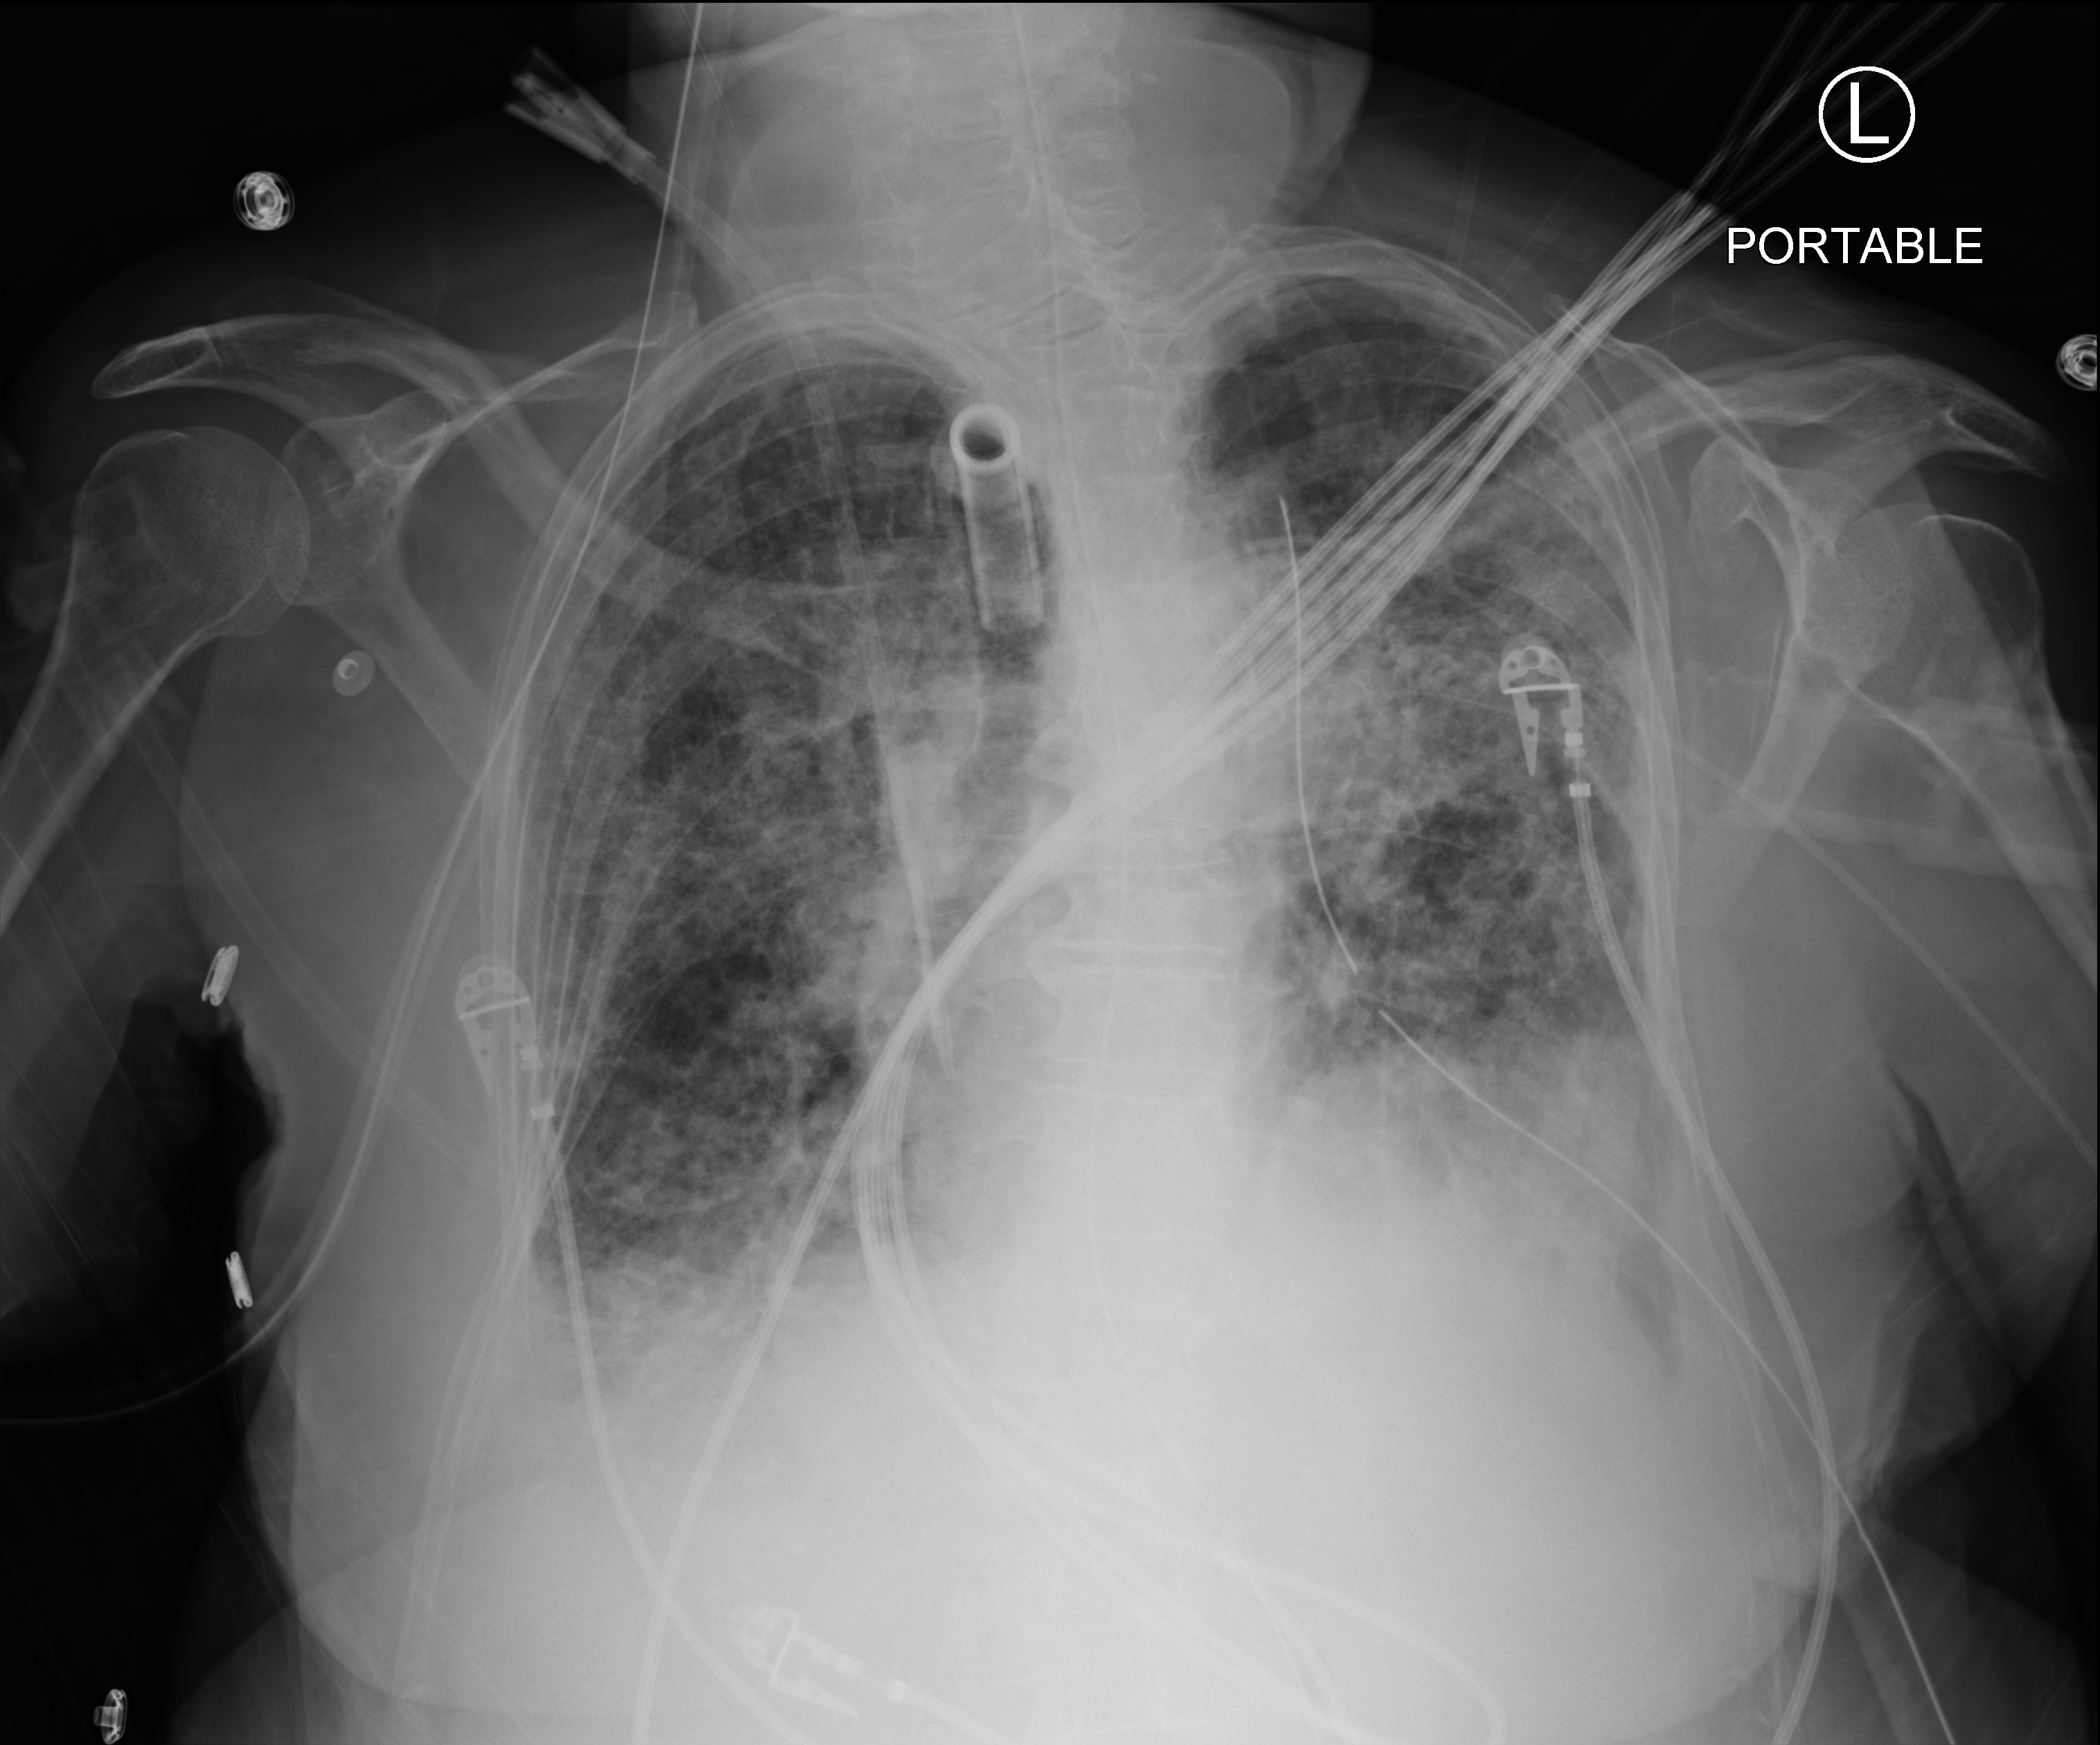
Bedside chest radiograph (computed radiography); anteroposterior (AP) projection. Female patient hospitalised with COVID-19, age 75–90 years.
From the hospital-stay record, not from the radiograph (when in the stay this image was taken is not recorded): admitted to intensive care during this hospital stay: yes; mechanically ventilated during this hospital stay: yes.